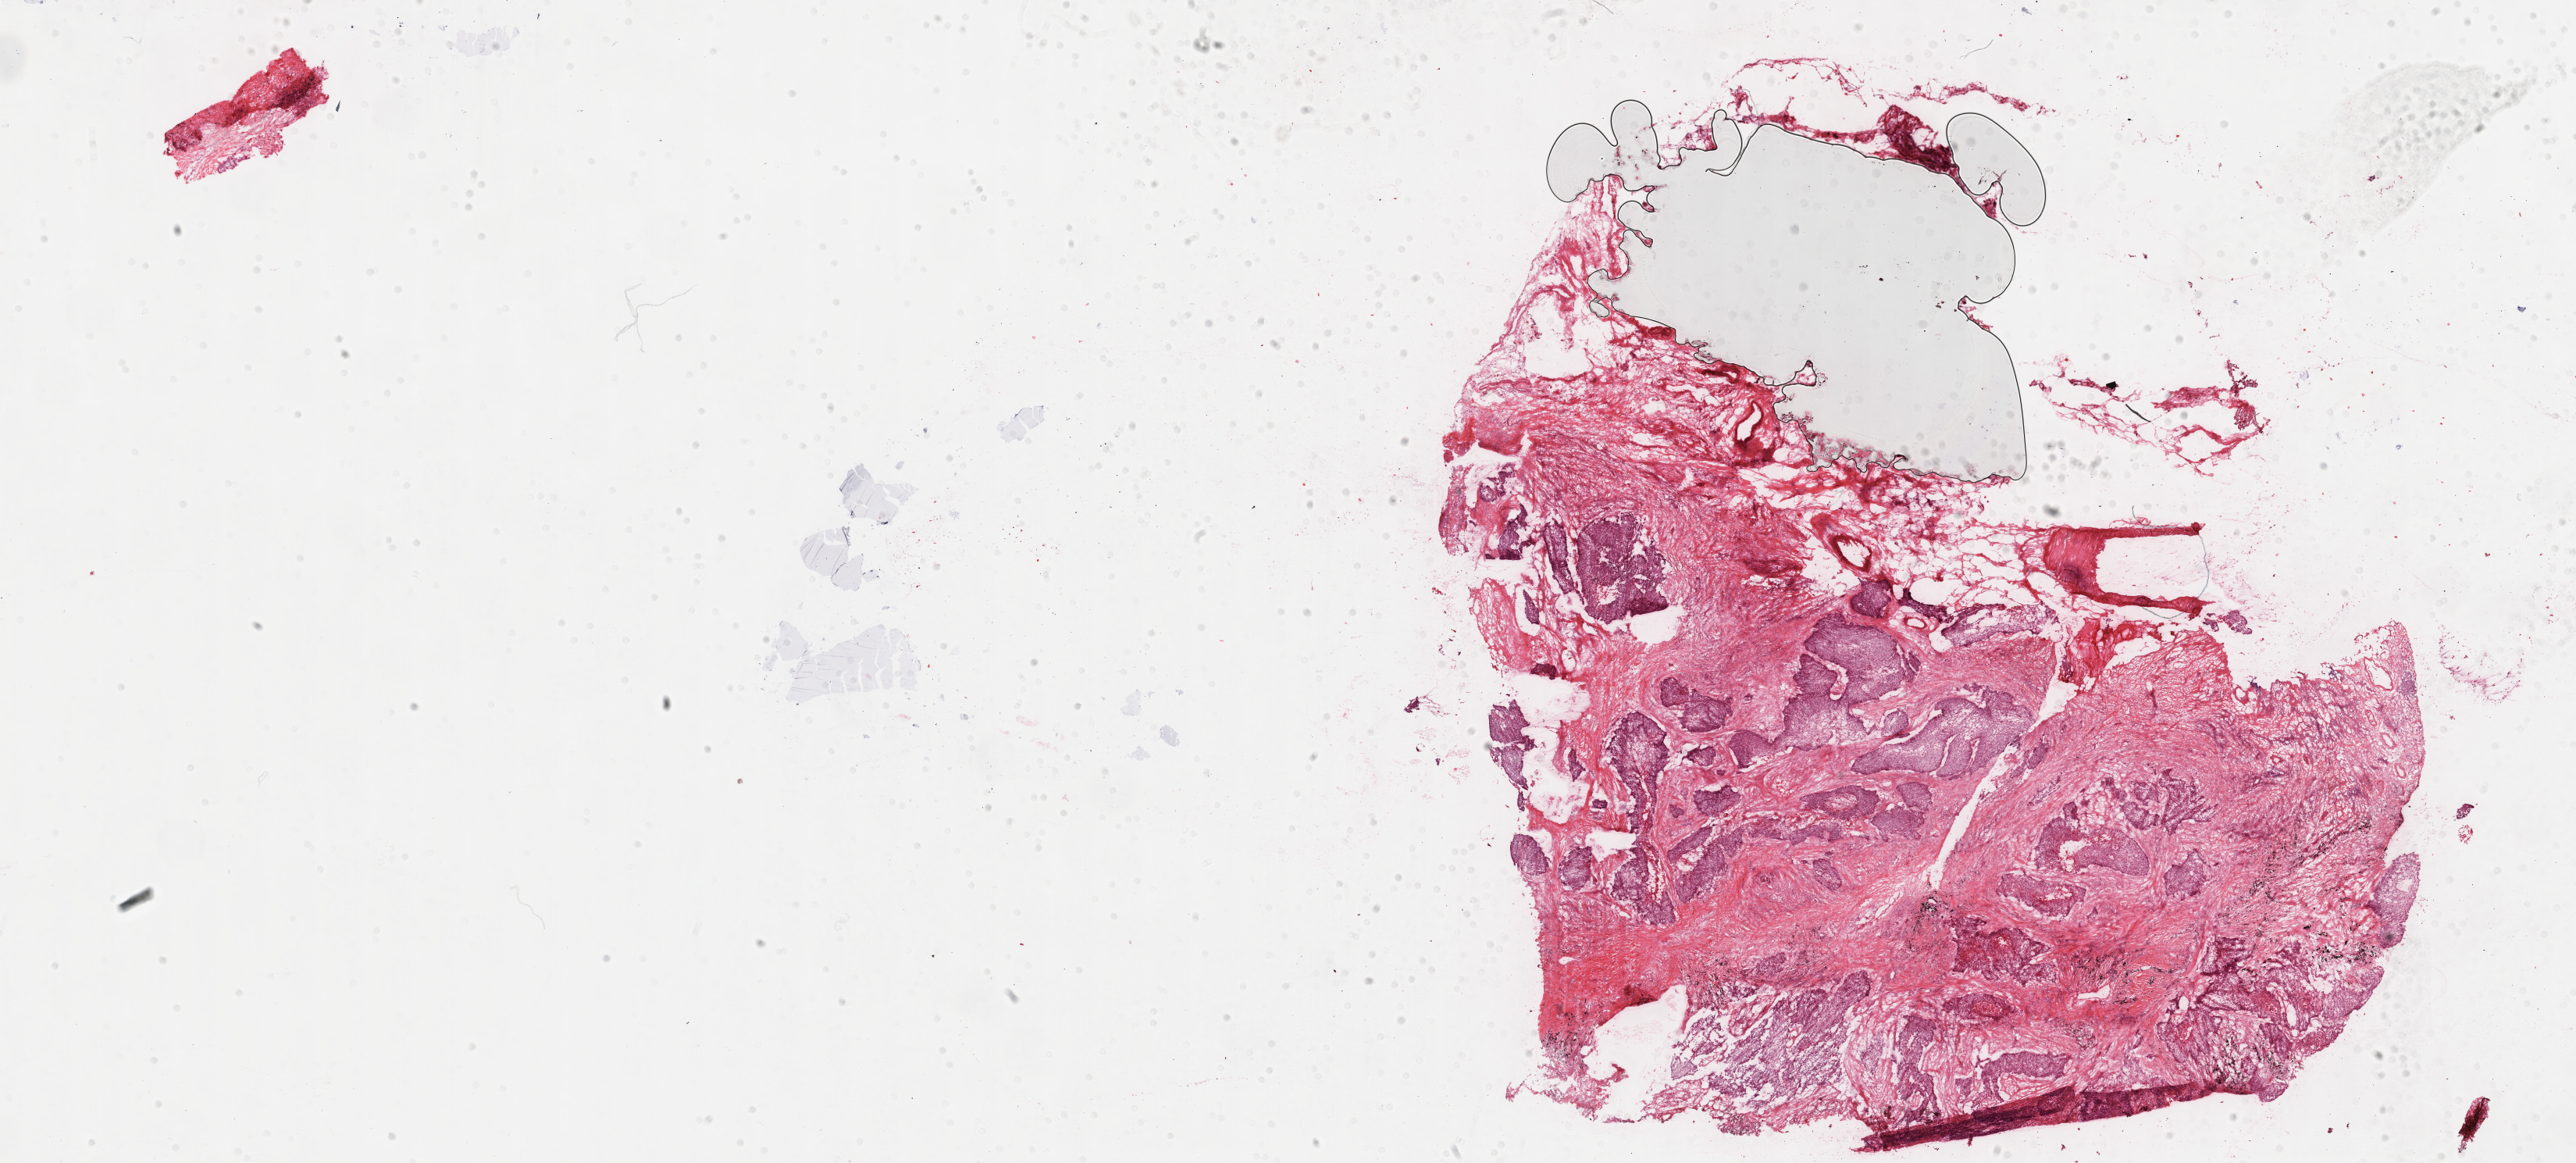
H&E-stained whole-slide image, a low-resolution overview of the entire scanned area, about 26.7 x 12.0 mm (from a 40x scan). Formalin-fixed paraffin-embedded (FFPE) diagnostic section. Primary tumour sample from the lung. Patient: male, age at initial diagnosis 70 years.
AJCC pathologic stage: II (7th edition). Pathologic diagnosis: Squamous cell carcinoma, NOS. Laterality: right.